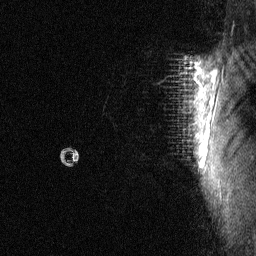
Breast MRI (dynamic contrast-enhanced), one sagittal slice; slice 53 of 64 in the series (ordered by position); dynamic contrast-enhanced study with each time point stored as its own series, time point 2 of 3 at this slice position (early post-contrast, ordered by acquisition time); 1.5 T; TE 4.8 ms, TR 27 ms; 256 × 256 image matrix, field of view 180 × 180 mm. Female patient, age 36 years. Case-level facts recorded for this patient, not image findings: setting: breast cancer imaged before/during neoadjuvant chemotherapy; receptor status: HR-positive, HER2-negative.
Annotated regions visible in this slice (semi-automatic segmentation, software-assisted and operator-edited):
- analysis volume of interest (the breast-tissue region the enhancement analysis was run in; not a lesion): box from (x=68, y=56) to (x=215, y=168) px
- tumour enhancement mask (voxels above the 90 % enhancement threshold inside the analysis volume of interest): (x=200, y=147)–(x=202, y=150)